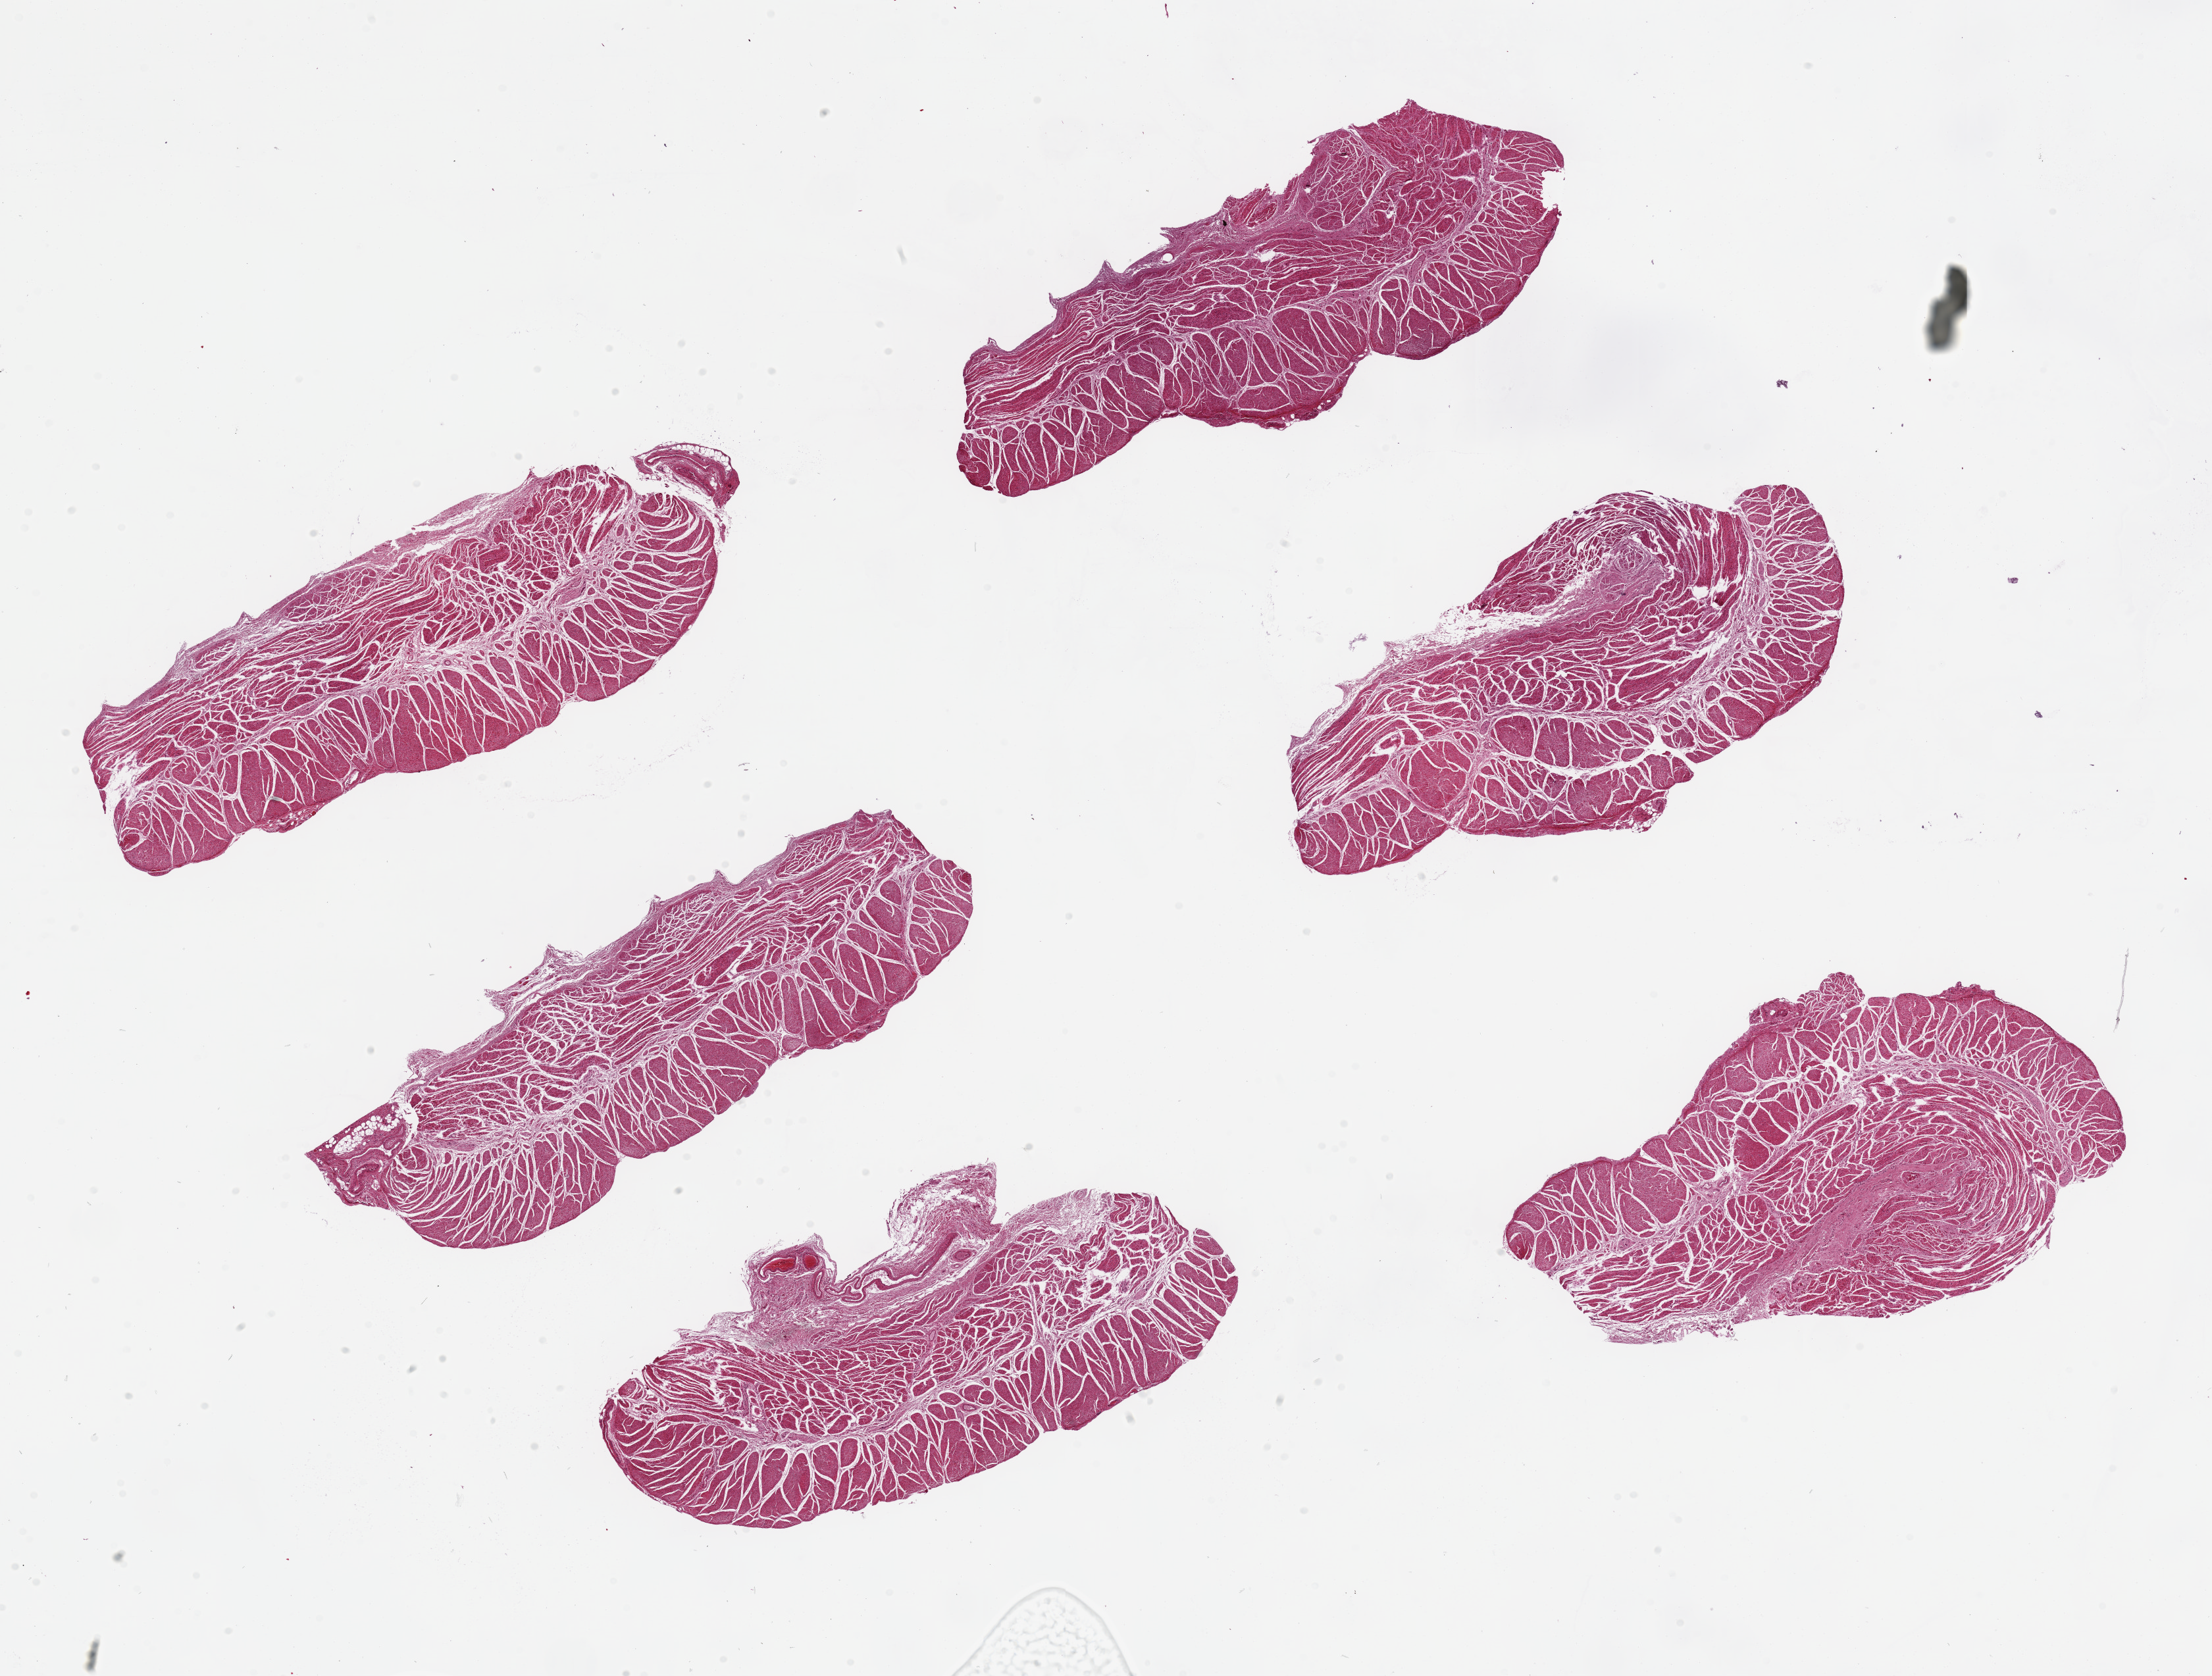
Digitized H&E-stained section — shown as a low-resolution overview of the whole scanned area (about 26.6 x 20.1 mm, slide scanned at 20x), PAXgene-fixed, paraffin-embedded tissue, section of esophageal muscle (target tissue), tissue donor sample. Donor sex: male.
Review note (as recorded): 6 ~8x3mm pieces.